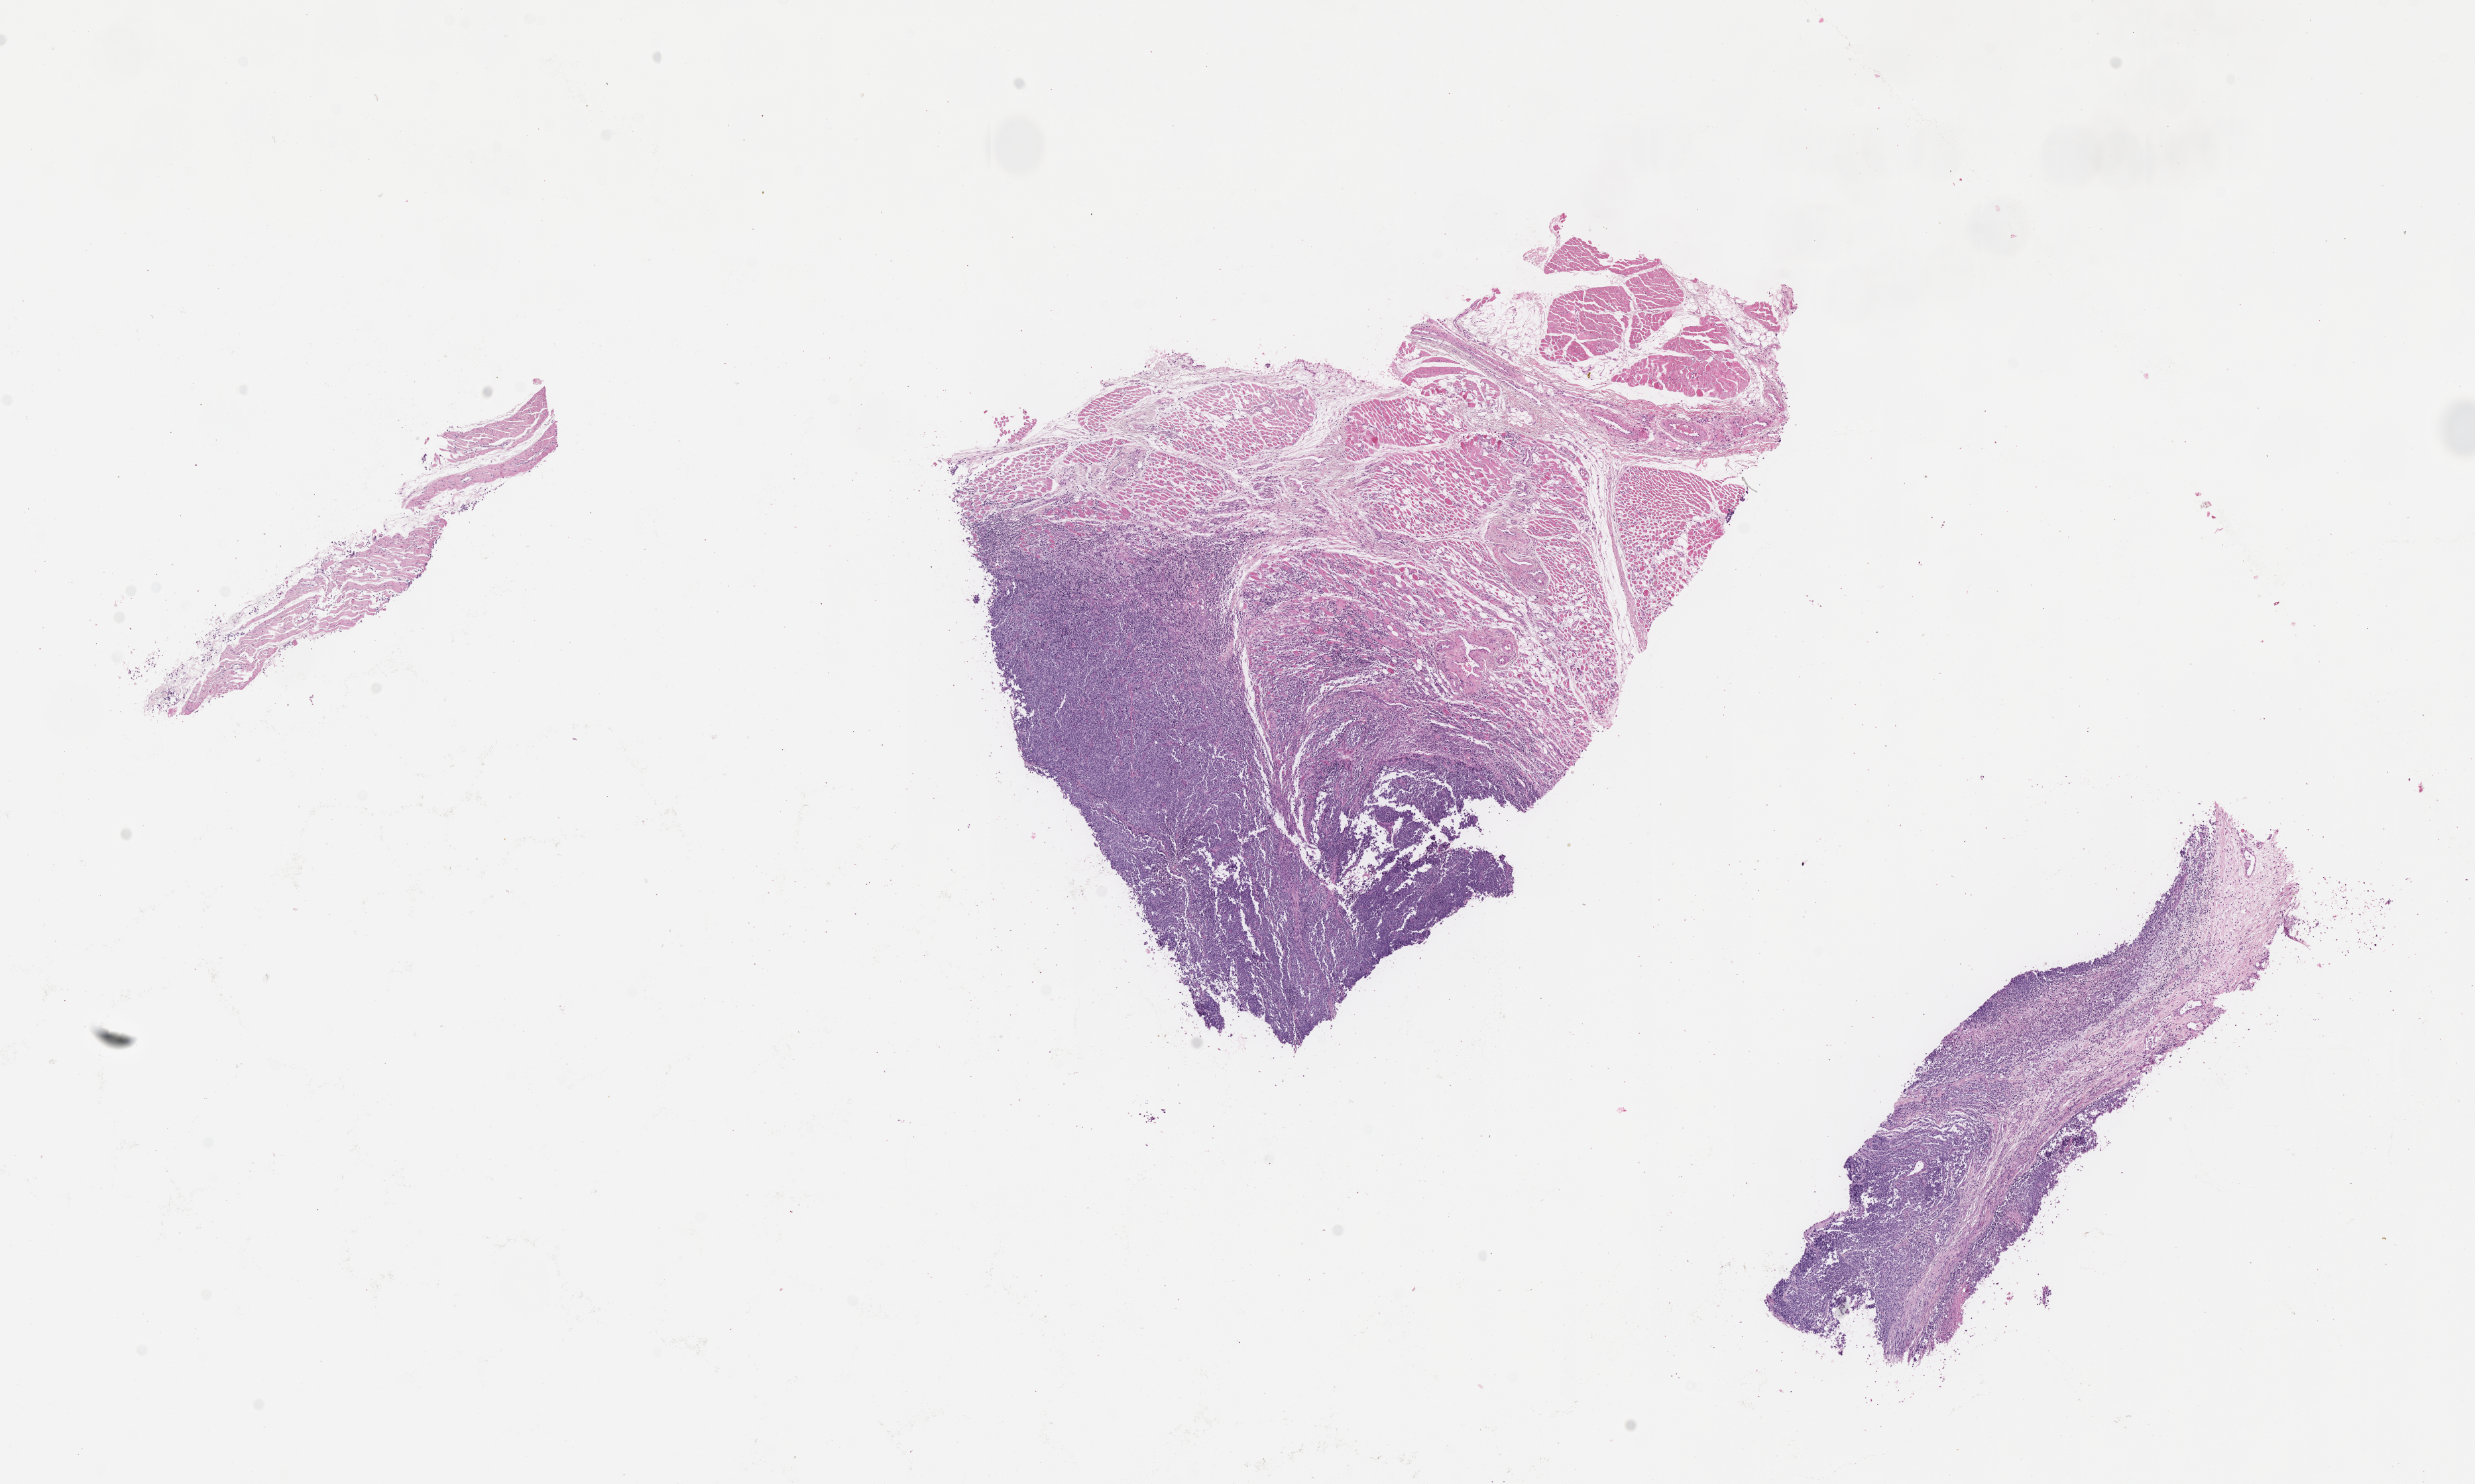
H&E whole-slide image of tumor tissue — shown as a low-resolution overview of the whole scanned area (about 15.1 x 9.1 mm). Formalin-fixed paraffin-embedded section. Sample anatomic site: leg, Left. Male patient, age at diagnosis 2.0 years.
Stage (as recorded): 2. Diagnosis: rhabdomyosarcoma; histological classification: alveolar rhabdomyosarcoma. Primary site (case record): thigh.